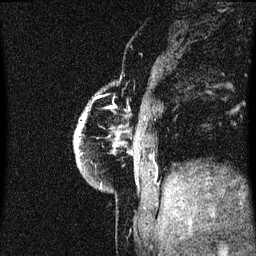
Breast MRI (dynamic contrast-enhanced), one sagittal slice. Slice 8 of 60 in the series (ordered by position). Dynamic contrast-enhanced series, image 2 of 3 at this slice position (ordered by acquisition). 1.5 T. TE 4.2 ms, TR 8.4 ms. 2 mm slice thickness. 256 × 256 image matrix, field of view 200 × 200 mm. Patient: female, 60 years.
Structures marked on this image (semi-automatic segmentation, software-assisted and operator-edited):
- analysis volume of interest (the breast-tissue region the enhancement analysis was run in; not a lesion): box from (x=74, y=92) to (x=103, y=187) px
- tumour enhancement mask (voxels above the 70 % enhancement threshold inside the analysis volume of interest): (x=74, y=120)–(x=85, y=165)